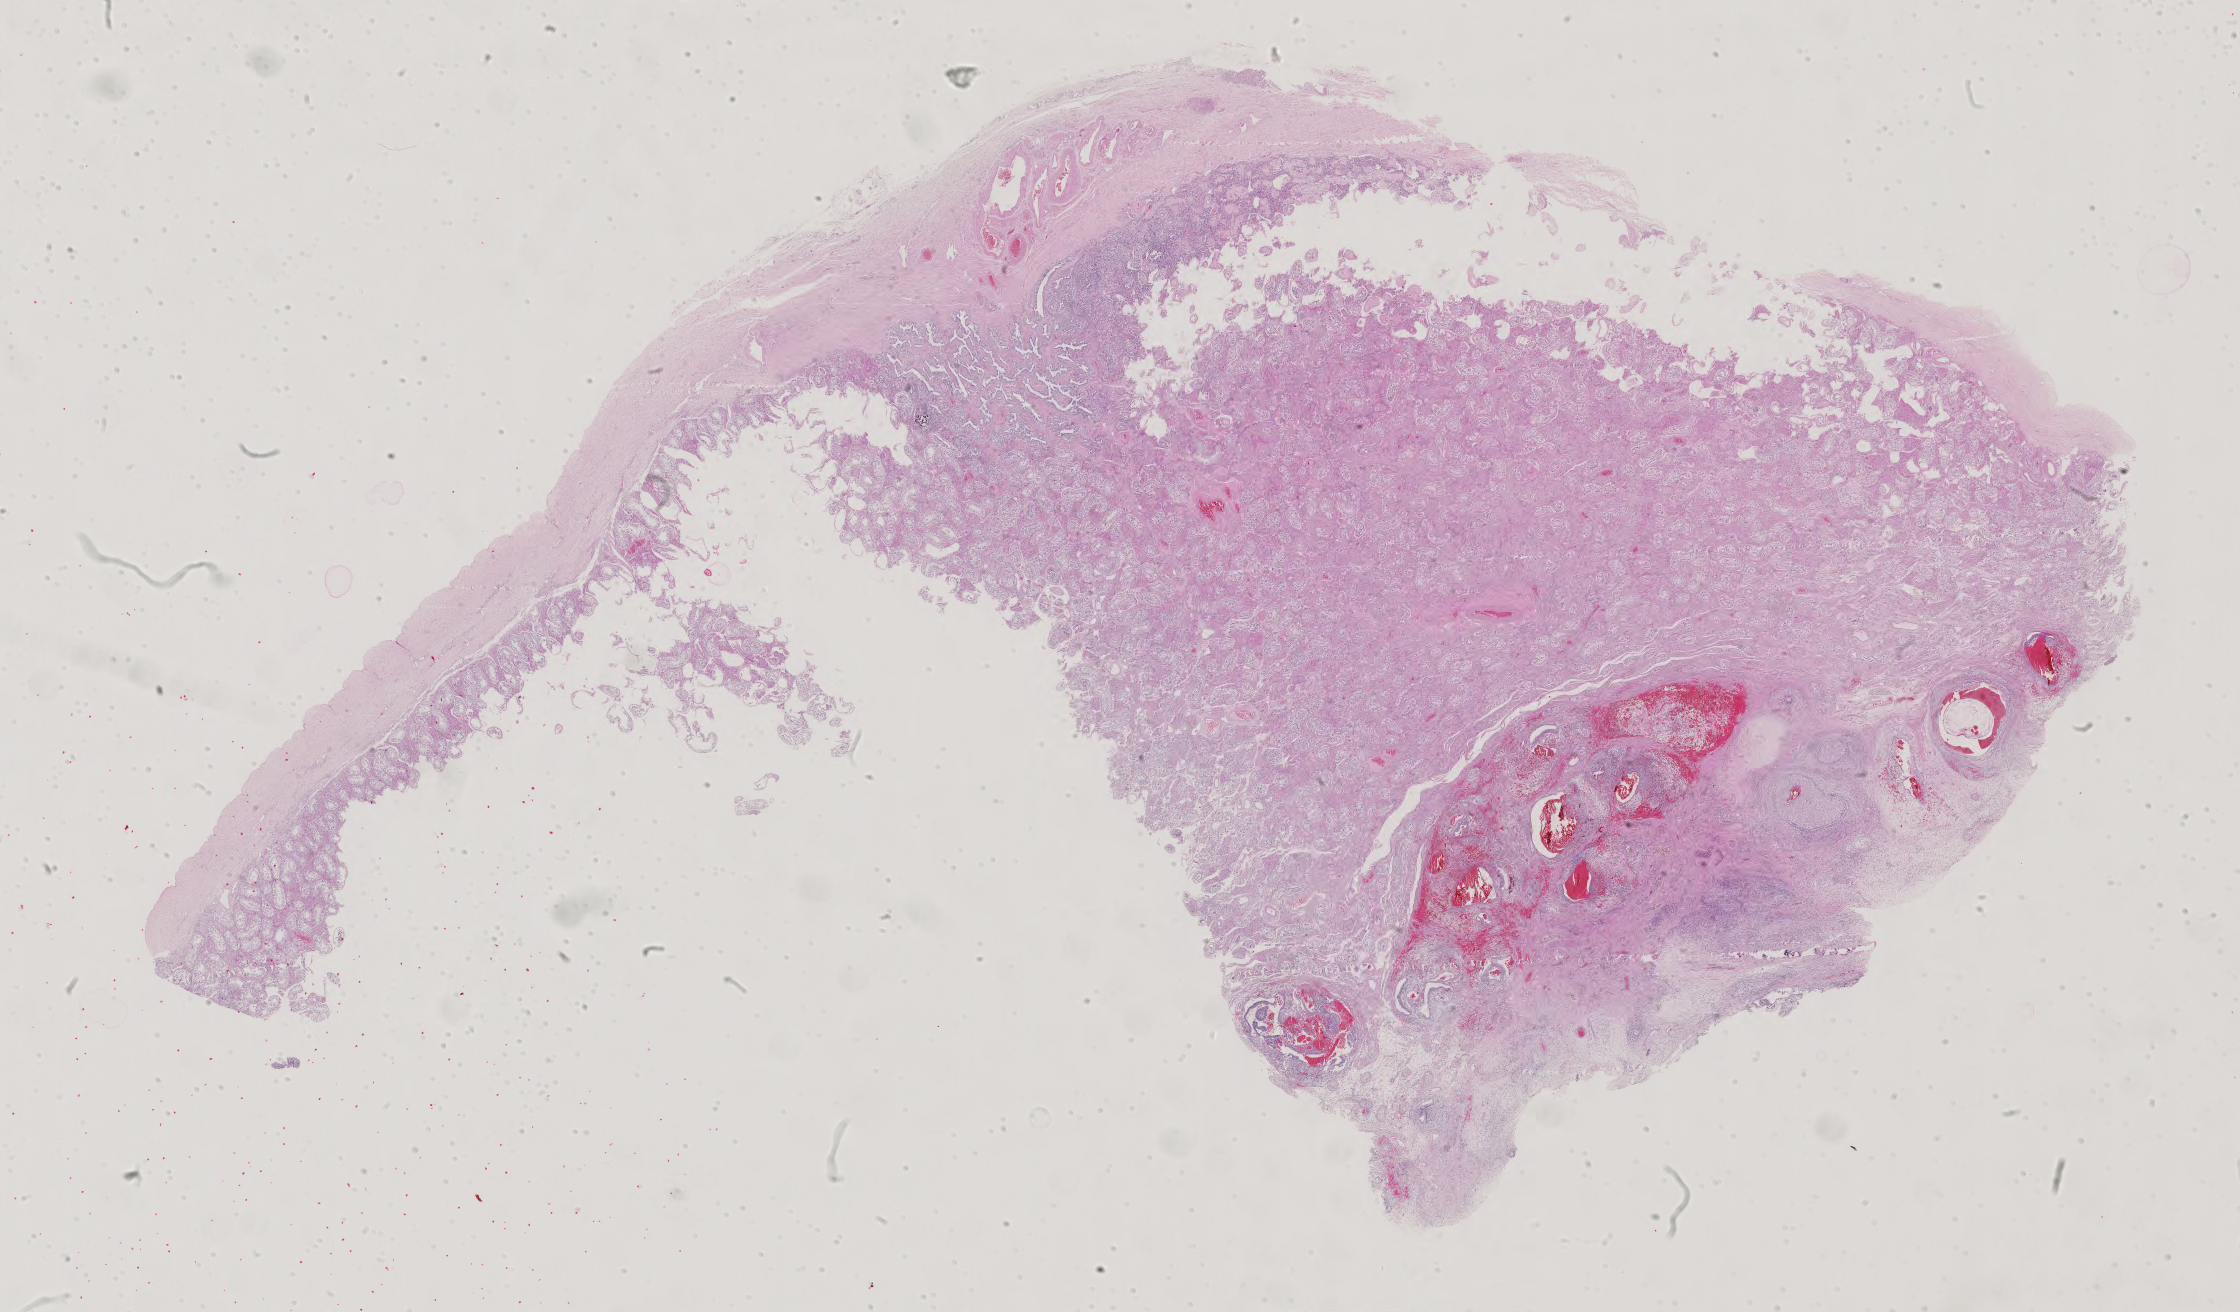
H&E-stained whole-slide image, low-resolution overview of the scanned area, about 32.6 x 19.1 mm, formalin-fixed paraffin-embedded (FFPE) diagnostic section, sample: primary tumour, testis. Male patient; age at initial diagnosis 33 years.
- laterality: right
- pathologic diagnosis: Mixed germ cell tumor
- AJCC pathologic stage: IS (6th edition)